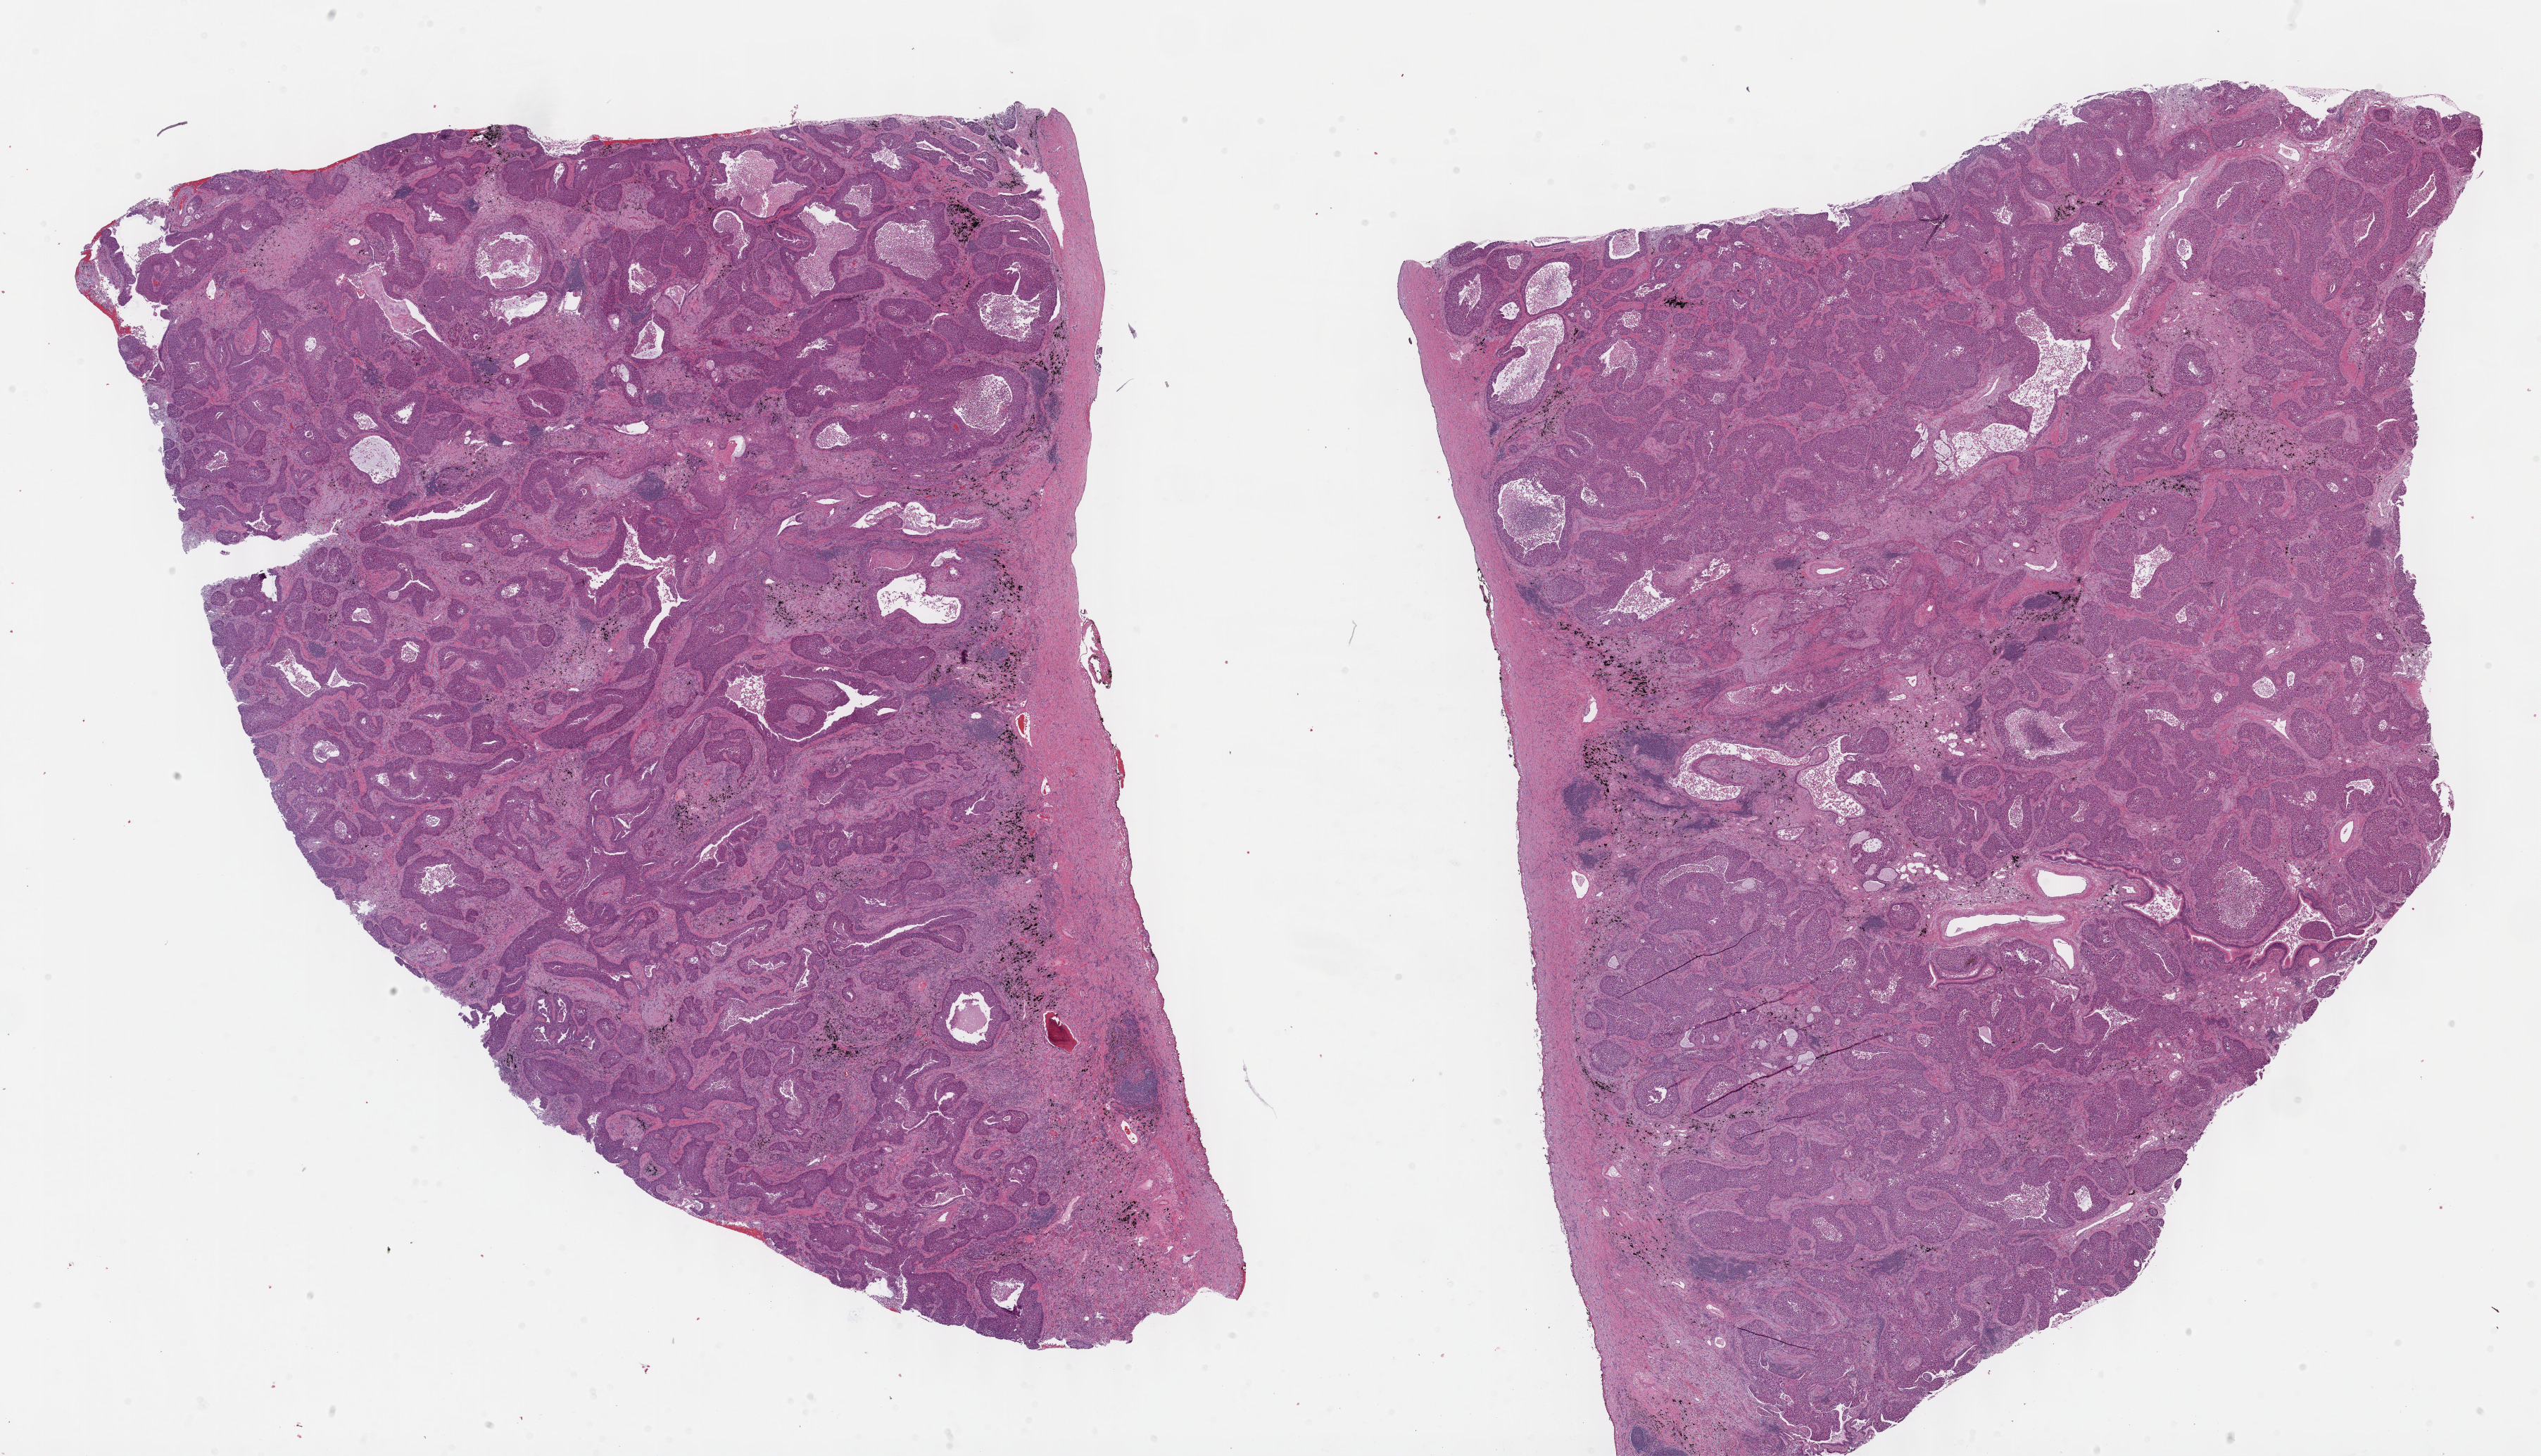
Whole-slide histology image, H&E — low-resolution overview of the scanned area, about 29.2 x 16.7 mm; formalin-fixed paraffin-embedded (FFPE) diagnostic section; sample: primary tumour, lung. Patient: male, age at initial diagnosis 75 years.
* pathologic diagnosis: Squamous cell carcinoma, NOS (lower lobe, lung)
* AJCC pathologic stage: IB
* laterality: right
* TNM: T2a N0 M0